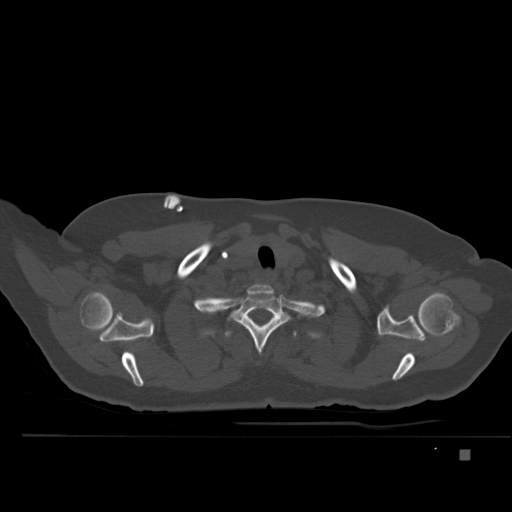
CT including the spine, one axial slice; slice 401 of 477 in the series (ordered by position); bone window (W 1800 / L 400 HU); 1.5 mm slice thickness; 512 × 512 image matrix, field of view 422 × 422 mm. Patient: female, 74 years. From the clinical record (not read from this slice): primary cancer: colon.
Outlined on this slice (semi-automatic segmentation, software-assisted and operator-edited):
- T1 vertebra: bounding box [x1, y1, x2, y2] px = [233, 293, 287, 352]
- T2 vertebra: [200, 320, 315, 339]